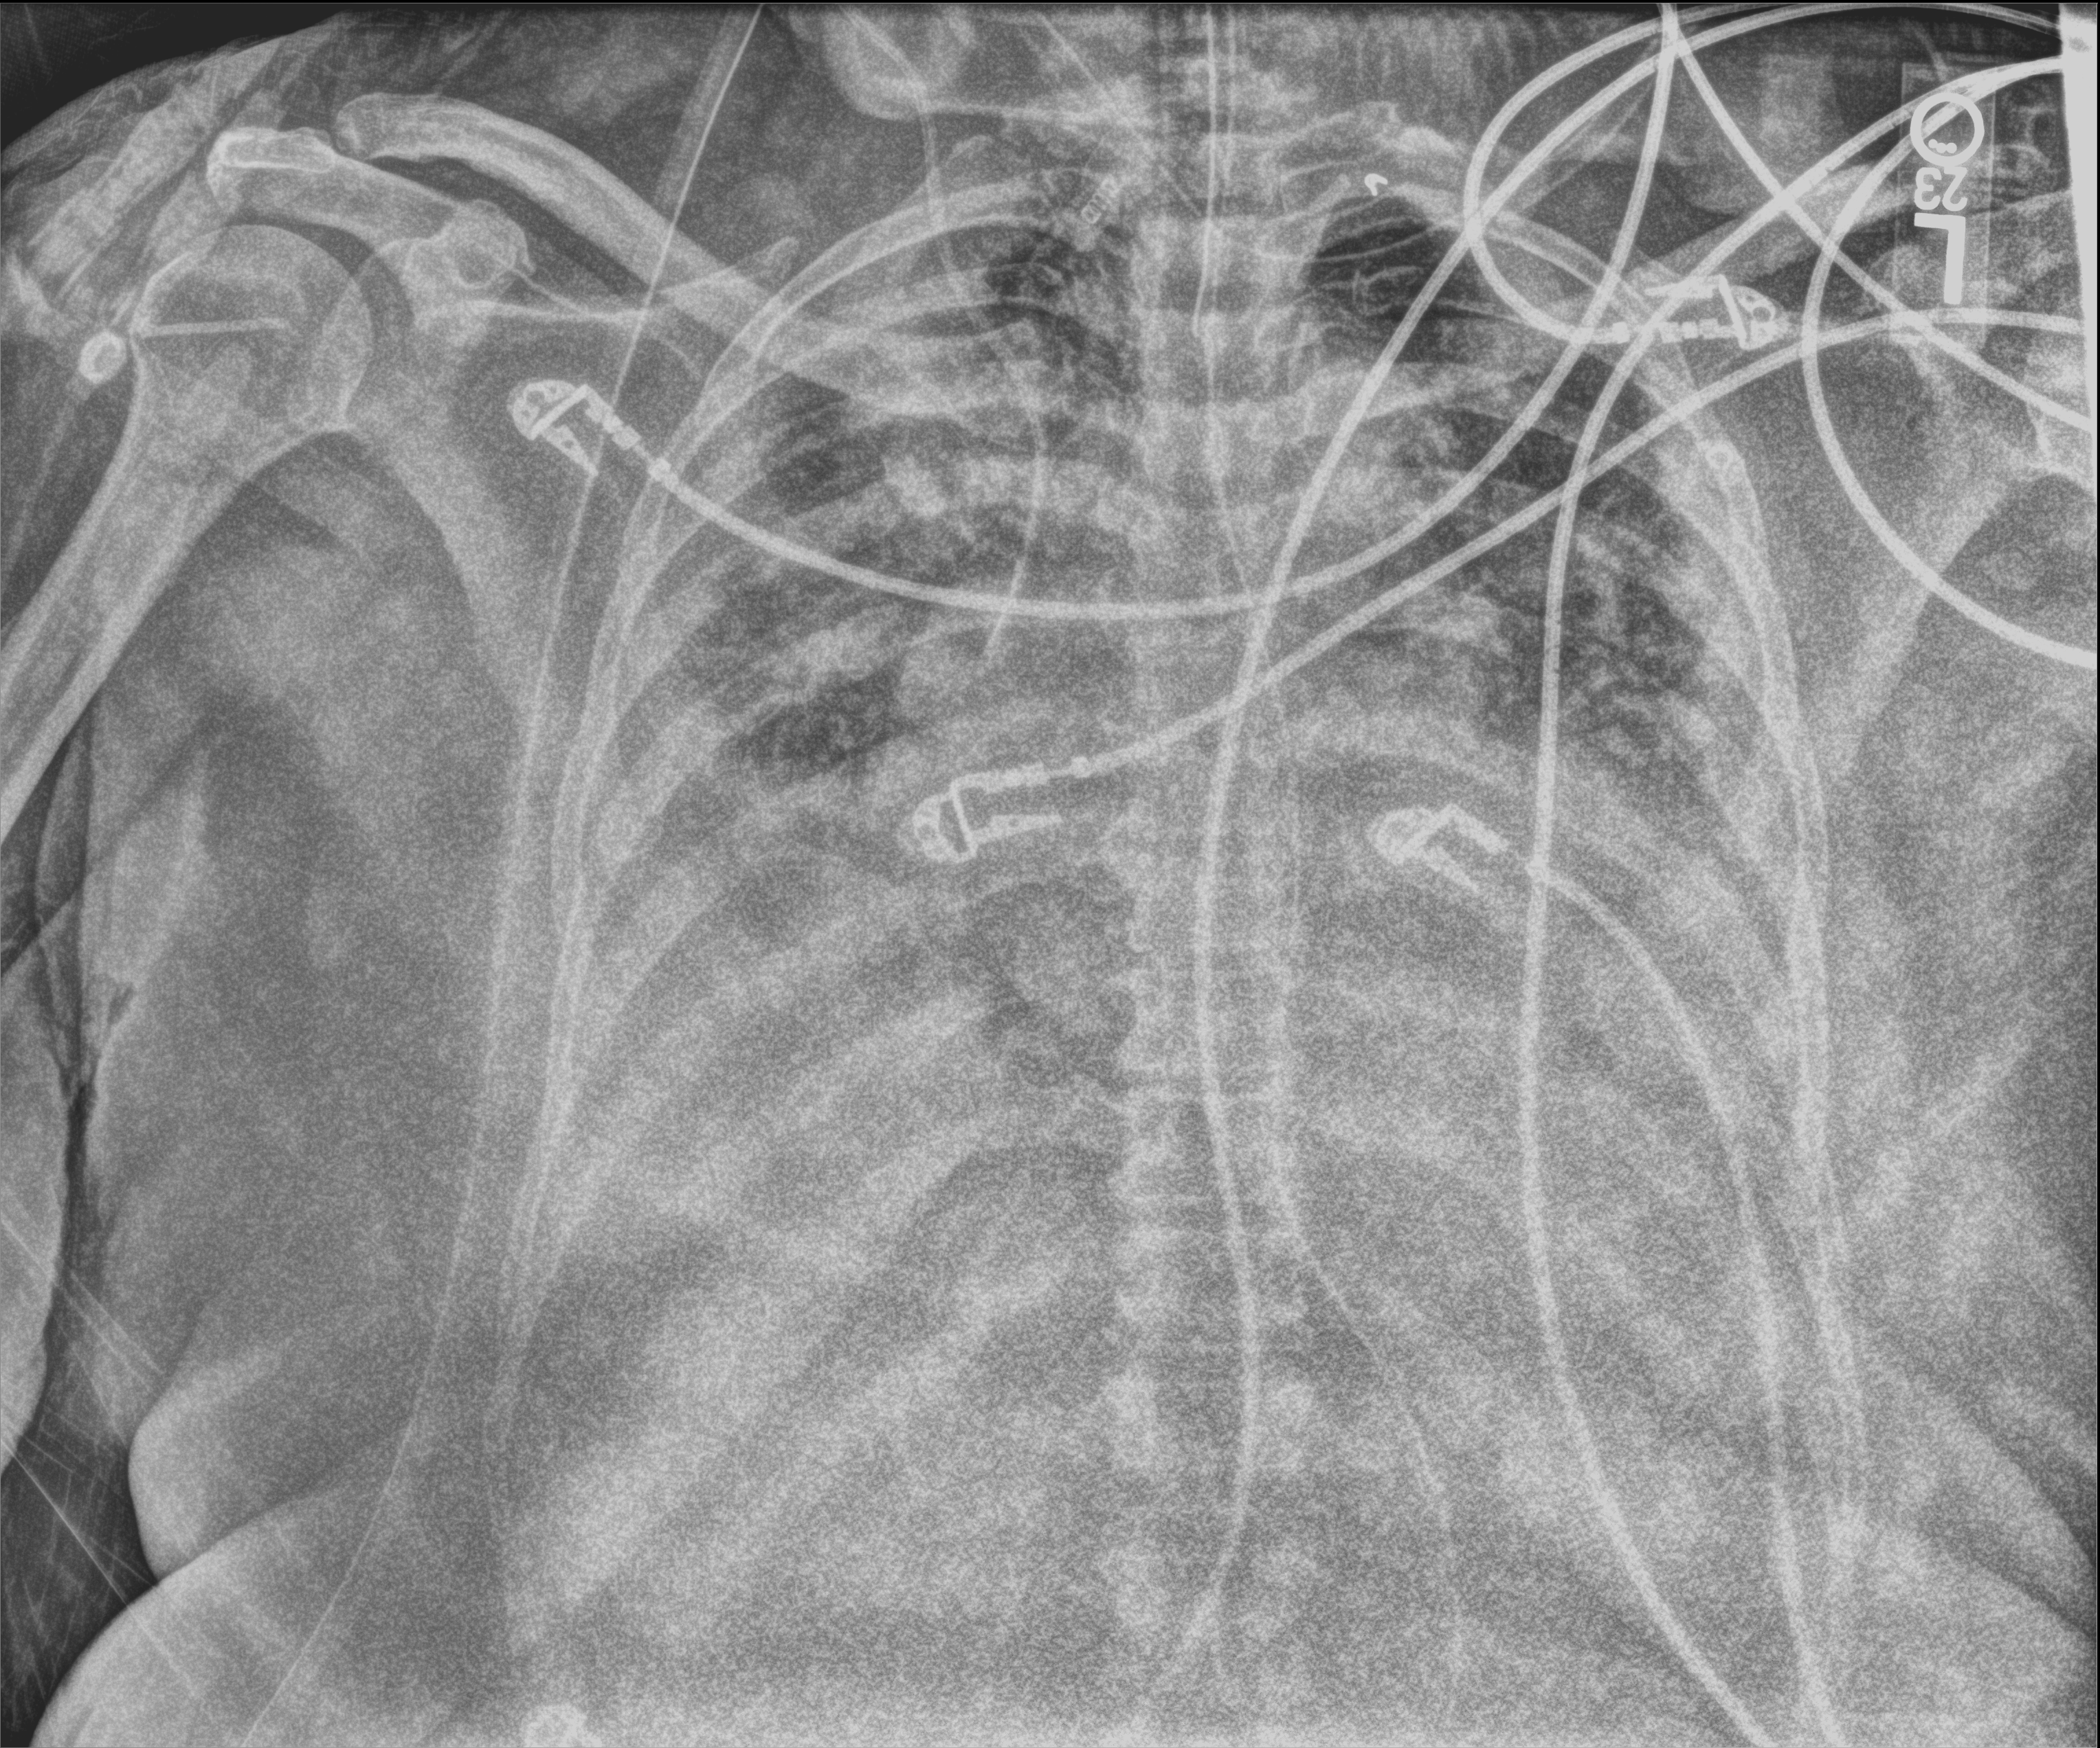
Portable chest radiograph; anteroposterior (AP) projection. Patient hospitalised with COVID-19; female, aged 60–74 years.
Admission-level facts for this patient (not findings on this image; timing relative to this image not recorded): COPD (admission record): no; admitted to intensive care during this hospital stay: yes.